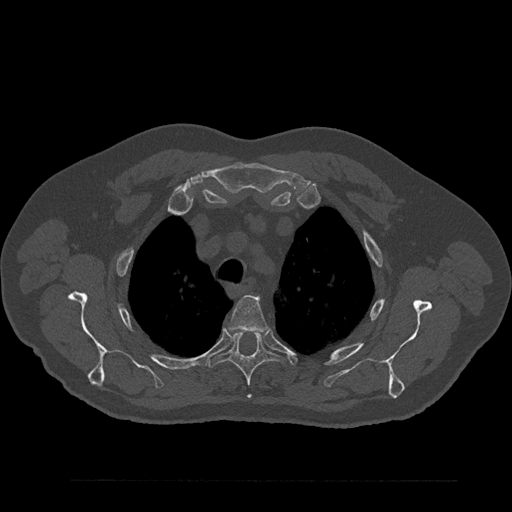
CT including the spine, one axial slice; slice 656 of 797 in the series (ordered by position); reconstruction kernel Br40s/3; bone window (W 1800 / L 400 HU); 512 × 512 image matrix, field of view 430 × 430 mm. Patient: male, 61 years. From the clinical record (not read from this slice): primary cancer: prostate.
Structures marked on this image (semi-automatic segmentation, software-assisted and operator-edited):
- T3 vertebra: box from (x=228, y=295) to (x=267, y=332) px
- T4 vertebra: (x=205, y=330)–(x=285, y=400)